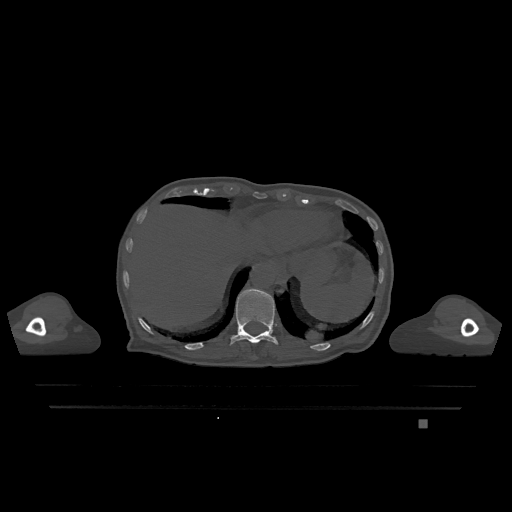
CT including the spine, one axial slice; position 589 of 1317 along the scan axis; bone window (W 1800 / L 400 HU); 512 × 512 image matrix, field of view 500 × 500 mm. Patient: female, 74 years. Case-level facts recorded for this patient, not image findings: primary cancer: lung; vertebrae with lytic lesions (as recorded): T1, T4, T5, T6, L4, L5.
Structures marked on this image (semi-automatically segmented with operator editing):
- T11 vertebra: bounding box (x1, y1, x2, y2) in pixels: (230, 289, 278, 345)